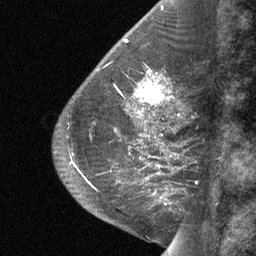
Breast MRI (dynamic contrast-enhanced), one sagittal slice. Slice 25 of 64 in the series (ordered by position). Dynamic contrast-enhanced study with each time point stored as its own series, time point 2 of 3 at this slice position (early post-contrast, ordered by acquisition time). 1.5 T. TE 4.8 ms, TR 27 ms. 2 mm slice thickness. 256 × 256 image matrix, field of view 180 × 180 mm. Female patient, age 59 years. Case-level facts recorded for this patient, not image findings: setting: breast cancer imaged before/during neoadjuvant chemotherapy; receptor status: triple-negative.
Annotated regions visible in this slice (semi-automatic segmentation, software-assisted and operator-edited):
- analysis volume of interest (the breast-tissue region the enhancement analysis was run in; not a lesion): bounding box (x1, y1, x2, y2) in pixels: (126, 75, 173, 114)
- tumour enhancement mask (voxels above the 90 % enhancement threshold inside the analysis volume of interest): (137, 80, 168, 106)